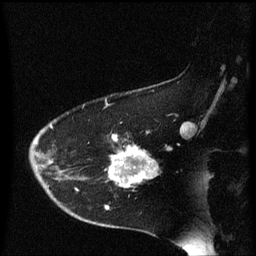
Breast MRI (dynamic contrast-enhanced), one sagittal slice; dynamic contrast-enhanced series, image 2 of 3 at this slice position (ordered by acquisition); 1.5 T; TE 4.2 ms, TR 8.4 ms; 2 mm slice thickness; 256 × 256 image matrix, field of view 200 × 200 mm. Patient: female, 54 years. From the clinical record (not read from this slice): setting: breast cancer imaged before/during neoadjuvant chemotherapy; receptor status: HR-positive, HER2-negative.
Outlined on this slice (semi-automatically segmented with operator editing):
- analysis volume of interest (the breast-tissue region the enhancement analysis was run in; not a lesion): bounding box (x1, y1, x2, y2) in pixels: (102, 132, 157, 197)
- tumour enhancement mask (voxels above the 70 % enhancement threshold inside the analysis volume of interest): (111, 146, 156, 189)